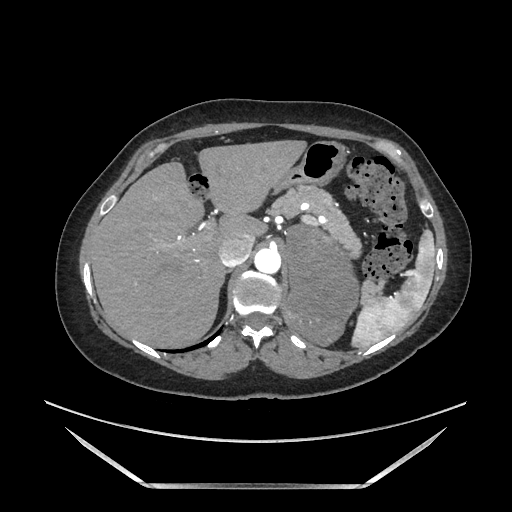
Contrast-enhanced abdominal CT, one axial slice; position 128 of 205 along the scan axis; soft-tissue window (W 400 / L 40 HU); 1.25 mm slice thickness; 512 × 512 image matrix. Female patient. From the clinical record (not read from this slice): diagnosis: adrenocortical carcinoma; tumour side: left adrenal; tumour size at pathology: 12.5 cm; Ki-67 index: 39 %; stage (as recorded): 3.
Structures marked on this image (semi-automatically segmented with operator editing):
- mass: bounding box (x1, y1, x2, y2) in pixels: (288, 225, 359, 345)